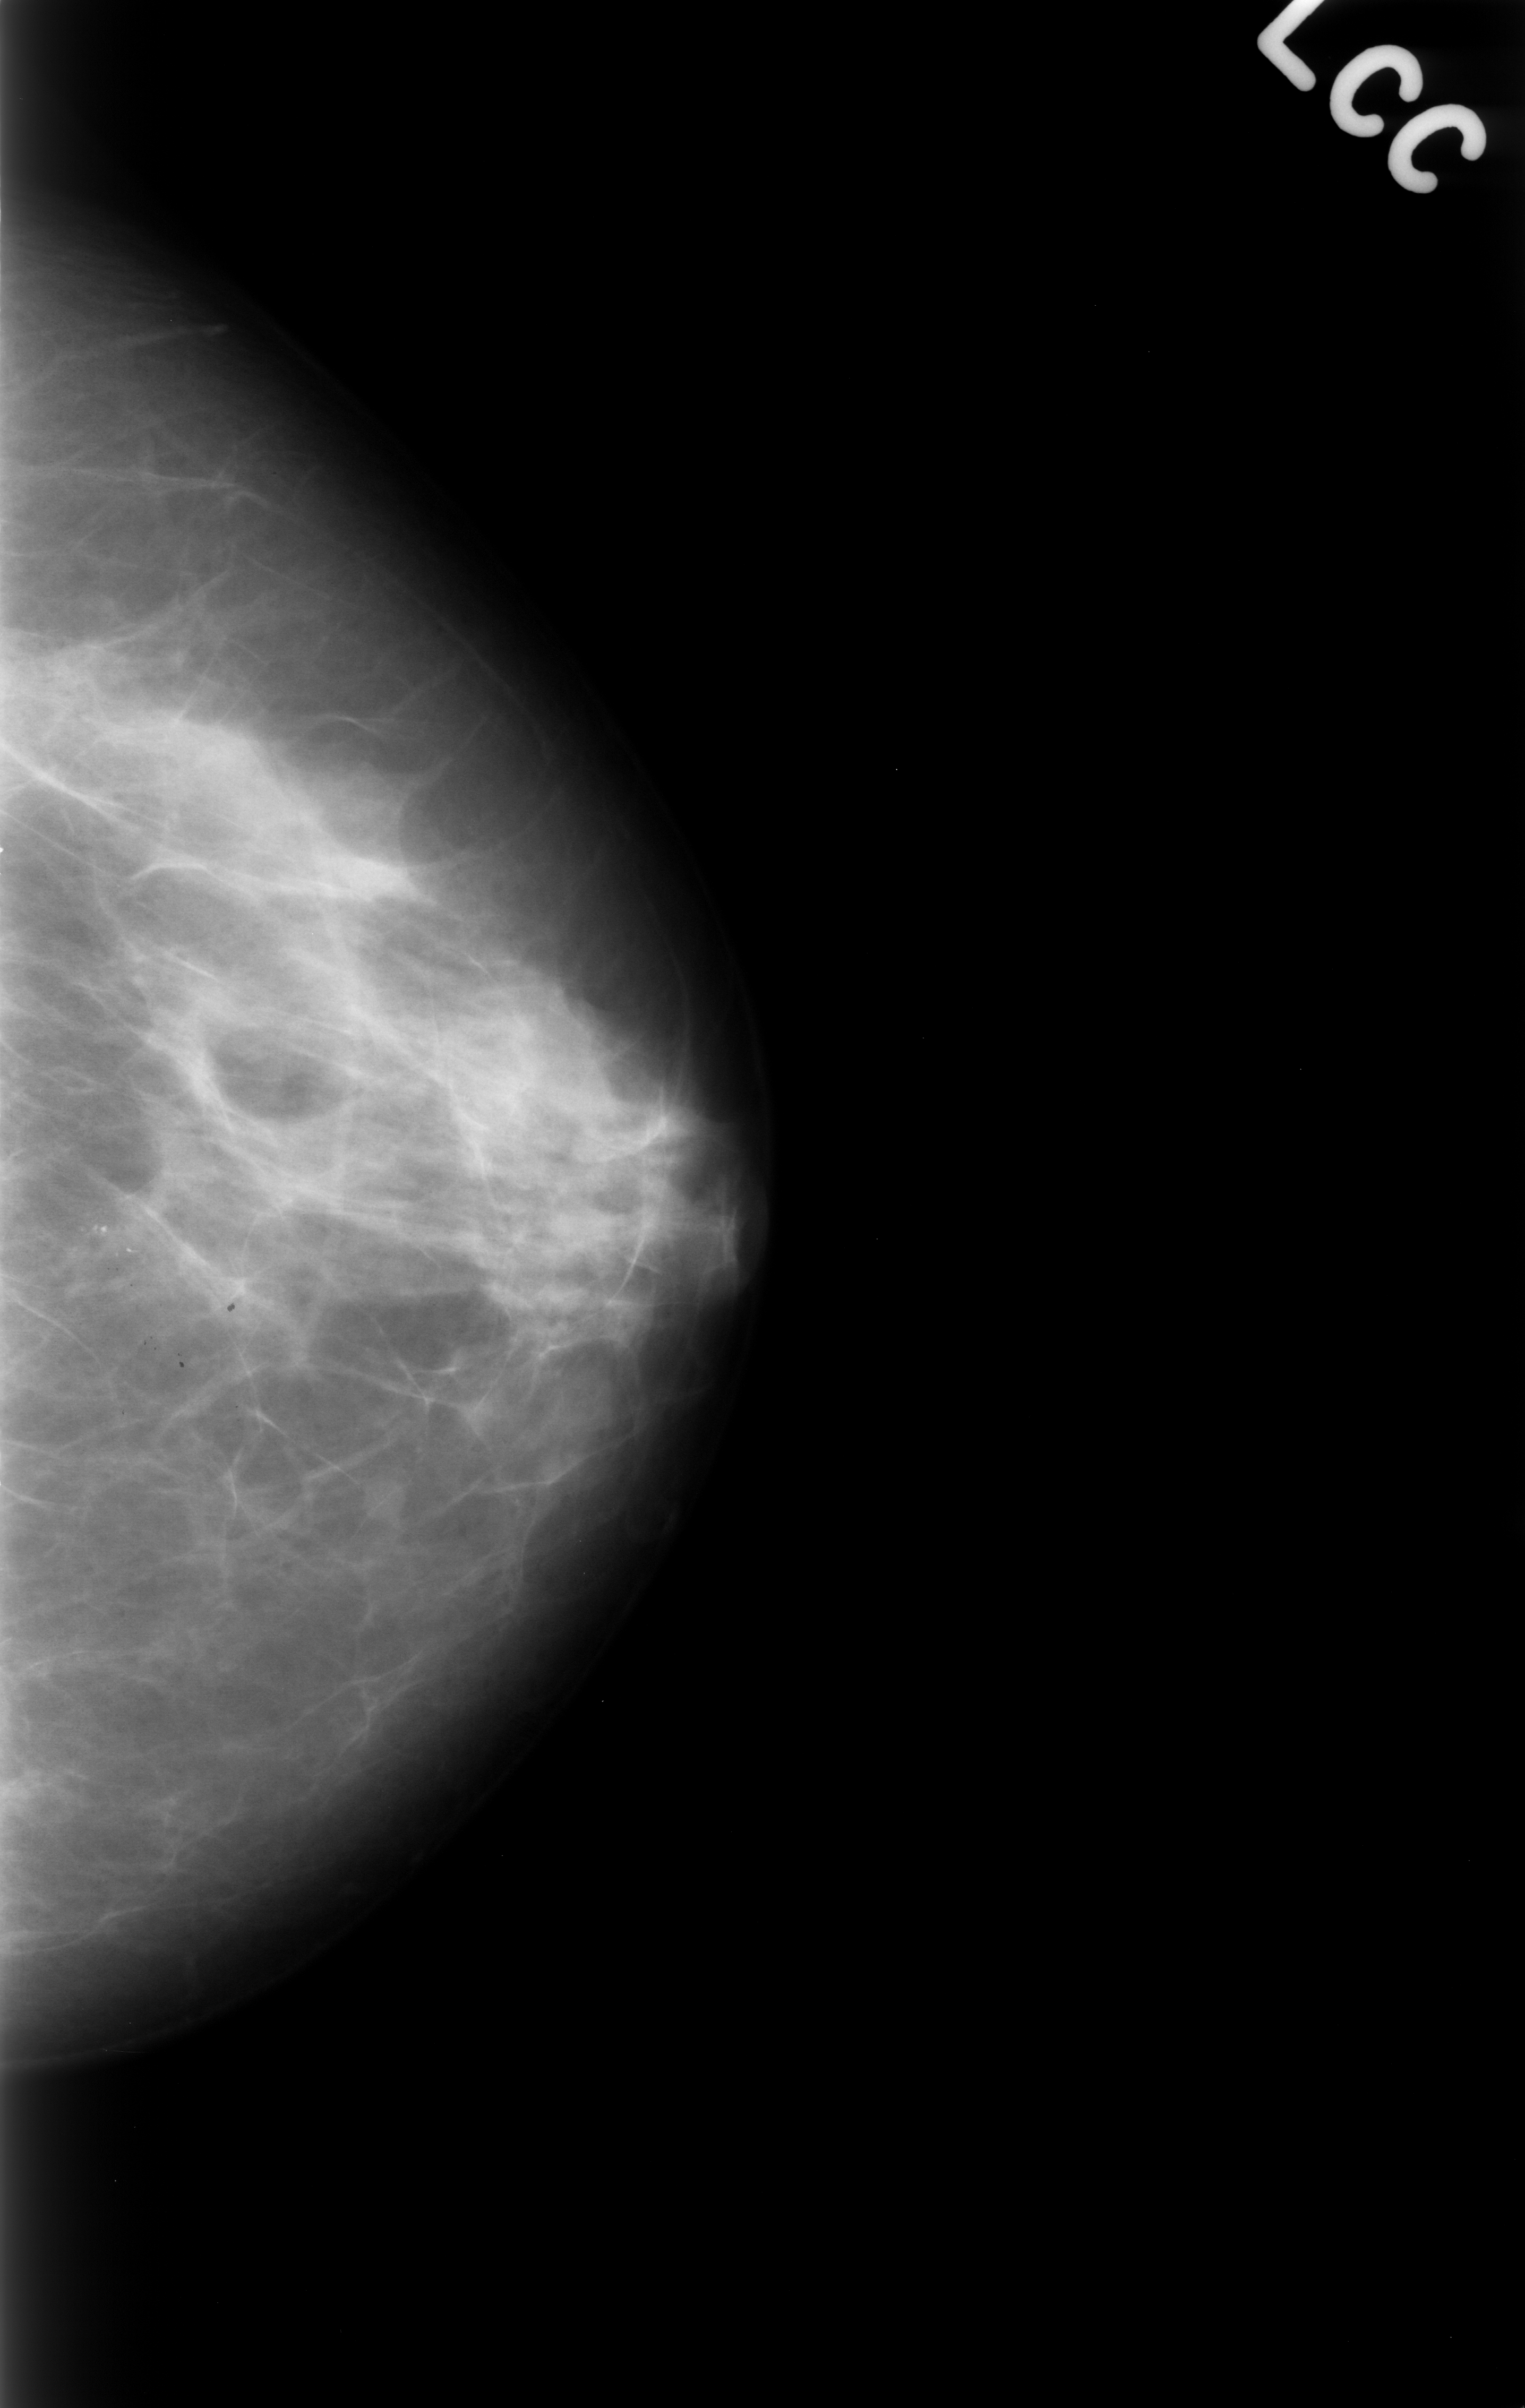
Mammogram (digitized film). Left breast. CC view. BI-RADS breast density category 2 (scale 1–4). 1525 × 2408 image matrix.
Expert-marked regions of interest on this image (one box per marked abnormality):
- calcifications, morphology punctate, distribution clustered; BI-RADS assessment category 4; subtlety rating 4 on a 1 (subtle) to 5 (obvious) scale; pathology (as recorded): benign: bounding box (x1, y1, x2, y2) in pixels: (16, 1159, 175, 1326)